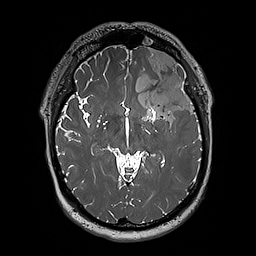
Brain MRI from a brain-tumour surgery series, one axial slice. Position 119 of 192 along the scan axis. 1 mm slice thickness. 256 × 256 image matrix, field of view 250 × 250 mm. Case-level facts recorded for this patient, not image findings: histopathology: Oligodendroglioma; WHO grade: 3.
Structures marked on this image (manually delineated by an expert):
- tumour: bounding box <124,50,197,122> (left, top, right, bottom; pixels)